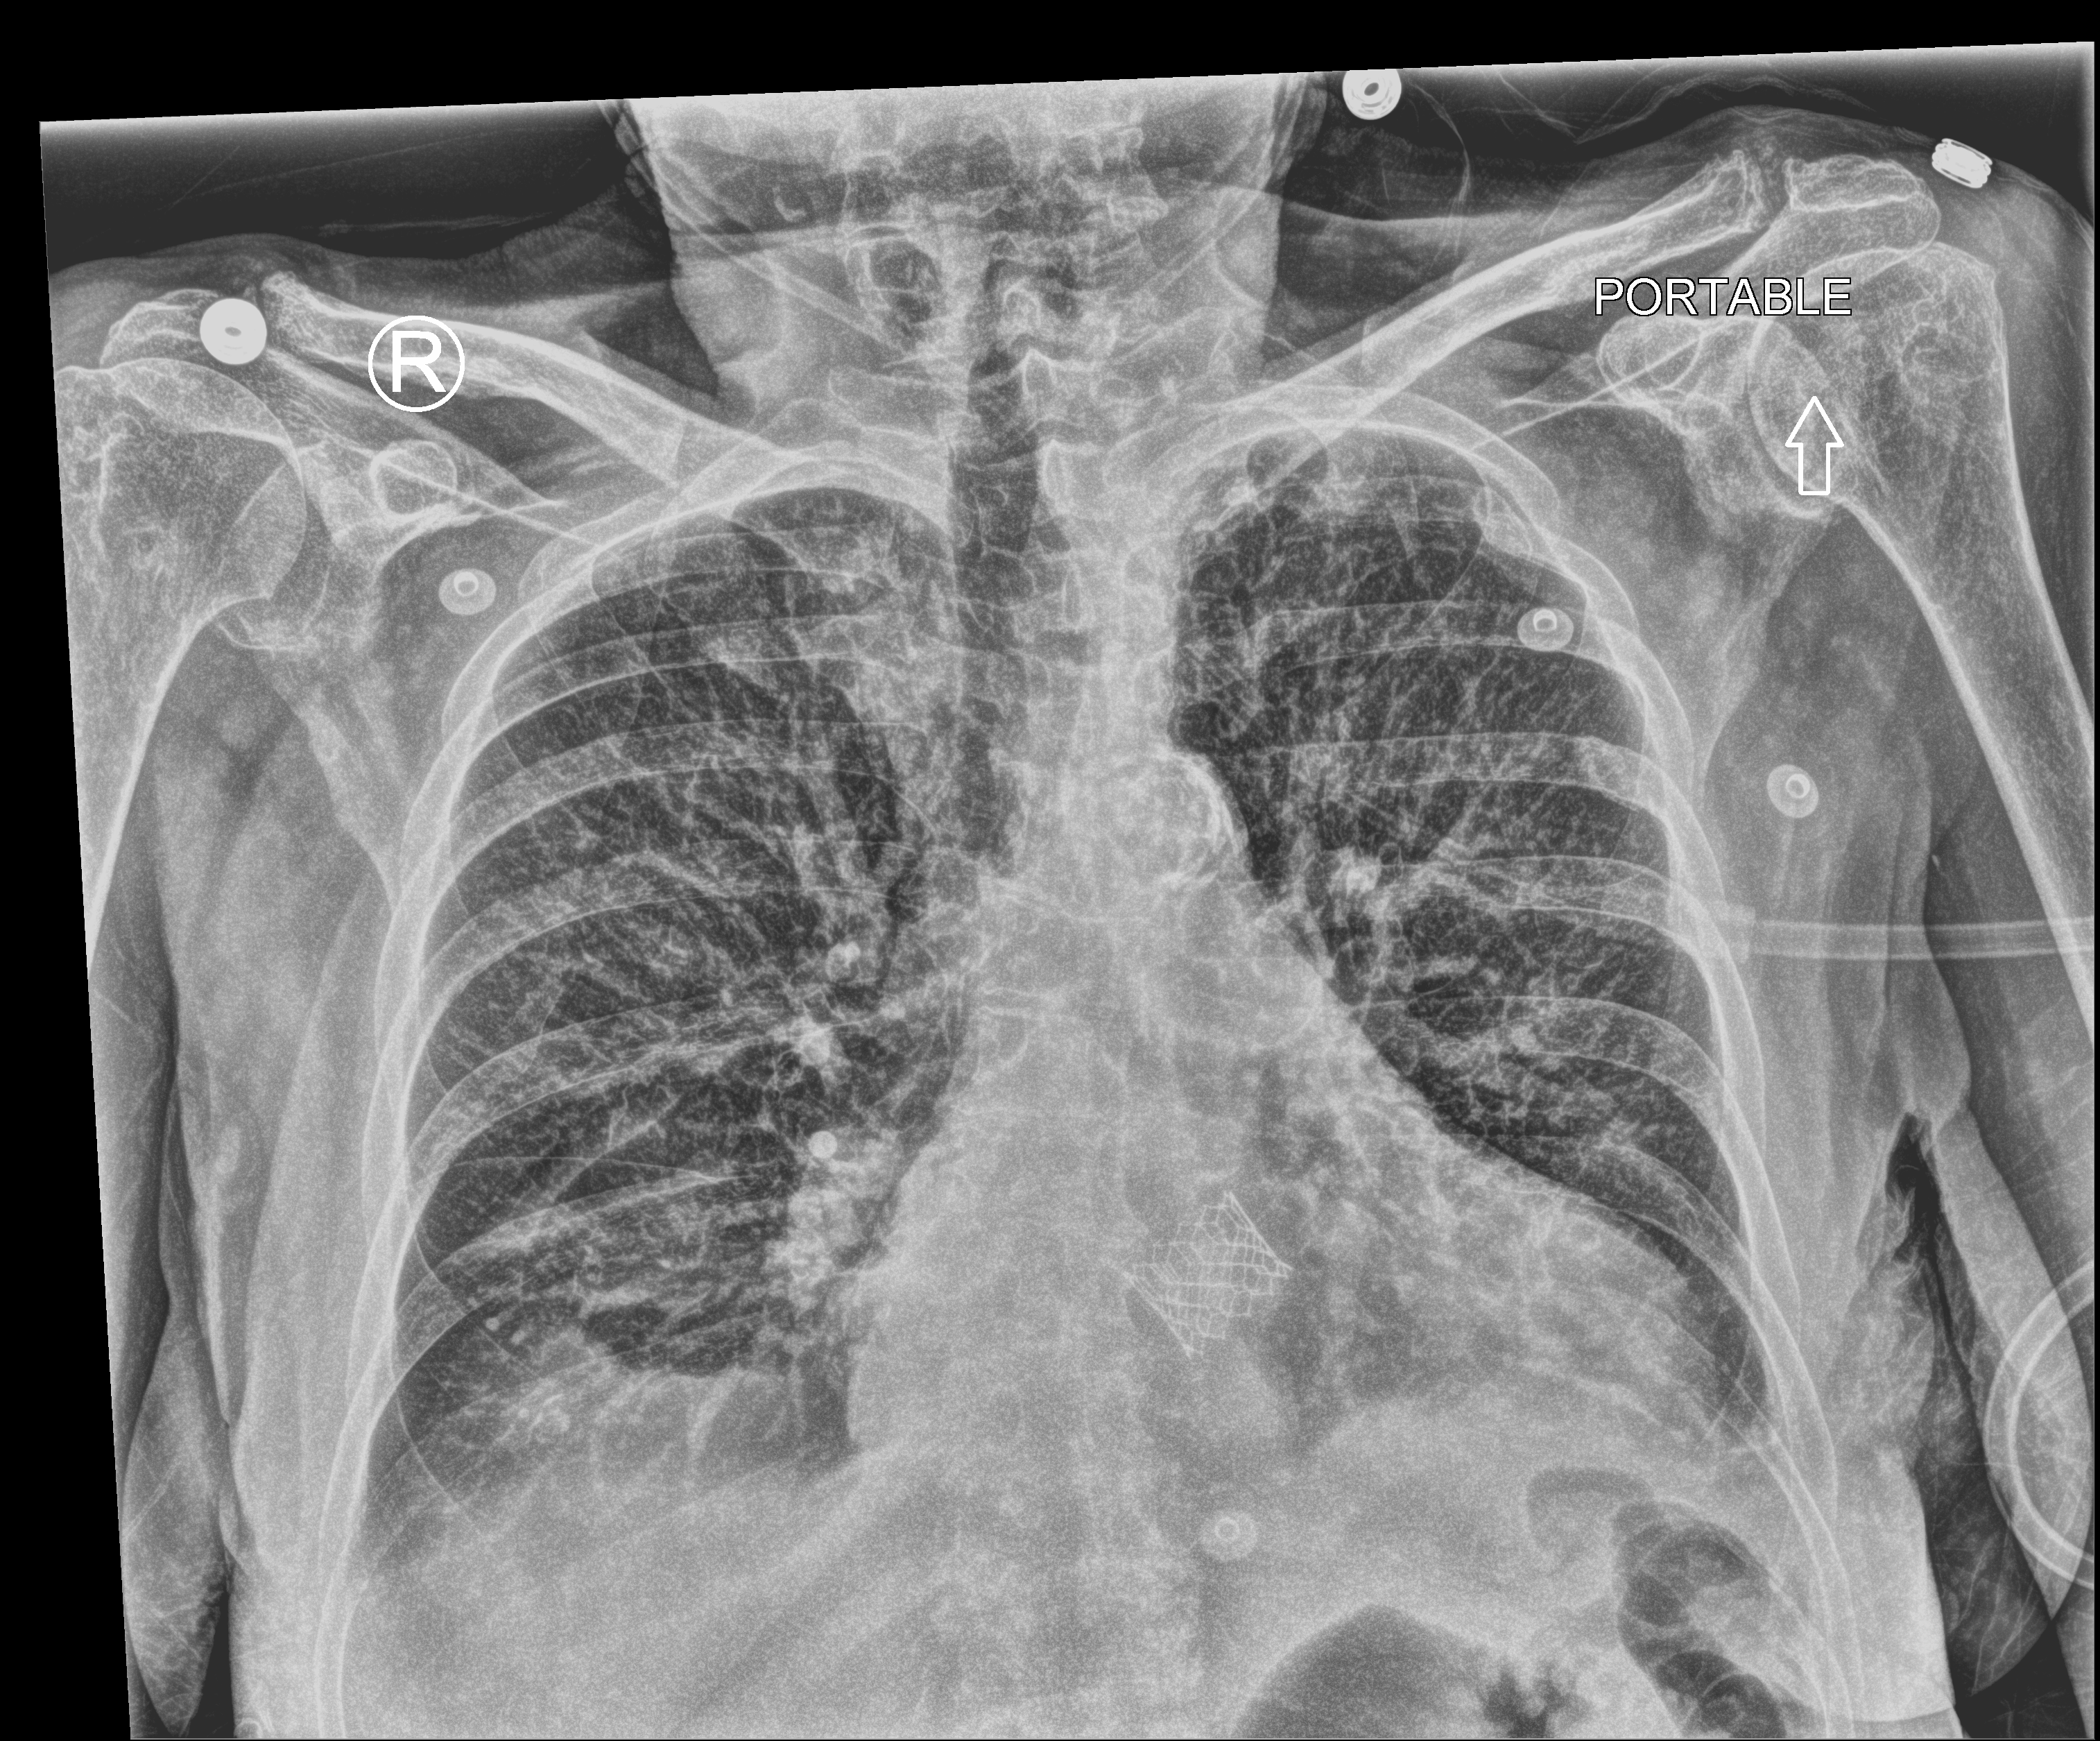
Bedside chest radiograph (computed radiography), anteroposterior (AP) projection. Female patient hospitalised with COVID-19, age 75–90 years.
Admission-level facts for this patient (not findings on this image; timing relative to this image not recorded): admitted to intensive care during this hospital stay: no.